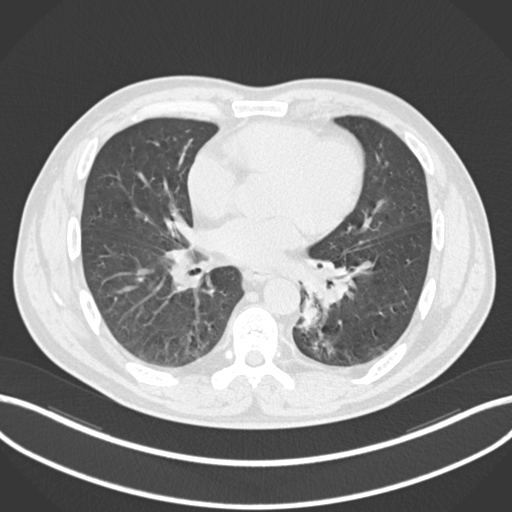
Chest CT, one axial slice; slice 100 of 223 in the series (ordered by position); reconstruction kernel B30f; lung window (W 1500 / L -600 HU); 1 mm slice thickness; 512 × 512 image matrix, field of view 400 × 400 mm. Patient: male, 50 years. From the clinical record (not read from this slice): clinical TNM (as recorded): T2a N3 M0.
Outlined on this slice (rectangle marked by the reading radiologist):
- lung tumour (recorded histology: squamous cell carcinoma): bounding box <298,298,320,333> (left, top, right, bottom; pixels)